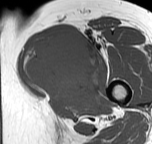
MRI of an extremity soft-tissue mass, one axial slice. Slice 39 of 57 in the series (ordered by position). MR volume resampled by the dataset authors to the PET/CT grid (not the native acquisition matrix). 3.27 mm slice thickness. 152 × 144 image matrix. Female patient. Case-level facts recorded for this patient, not image findings: histological type: pleiomorphic leiomyosarcoma; grade: intermediate; site of the primary tumour: left thigh.
Outlined on this slice (expert contour drawn on MRI and transferred to this co-registered scan by the dataset authors):
- gross tumour volume including surrounding oedema: bounding box <22,30,103,95> (left, top, right, bottom; pixels)
- gross tumour volume (mass): <22,30,103,95>